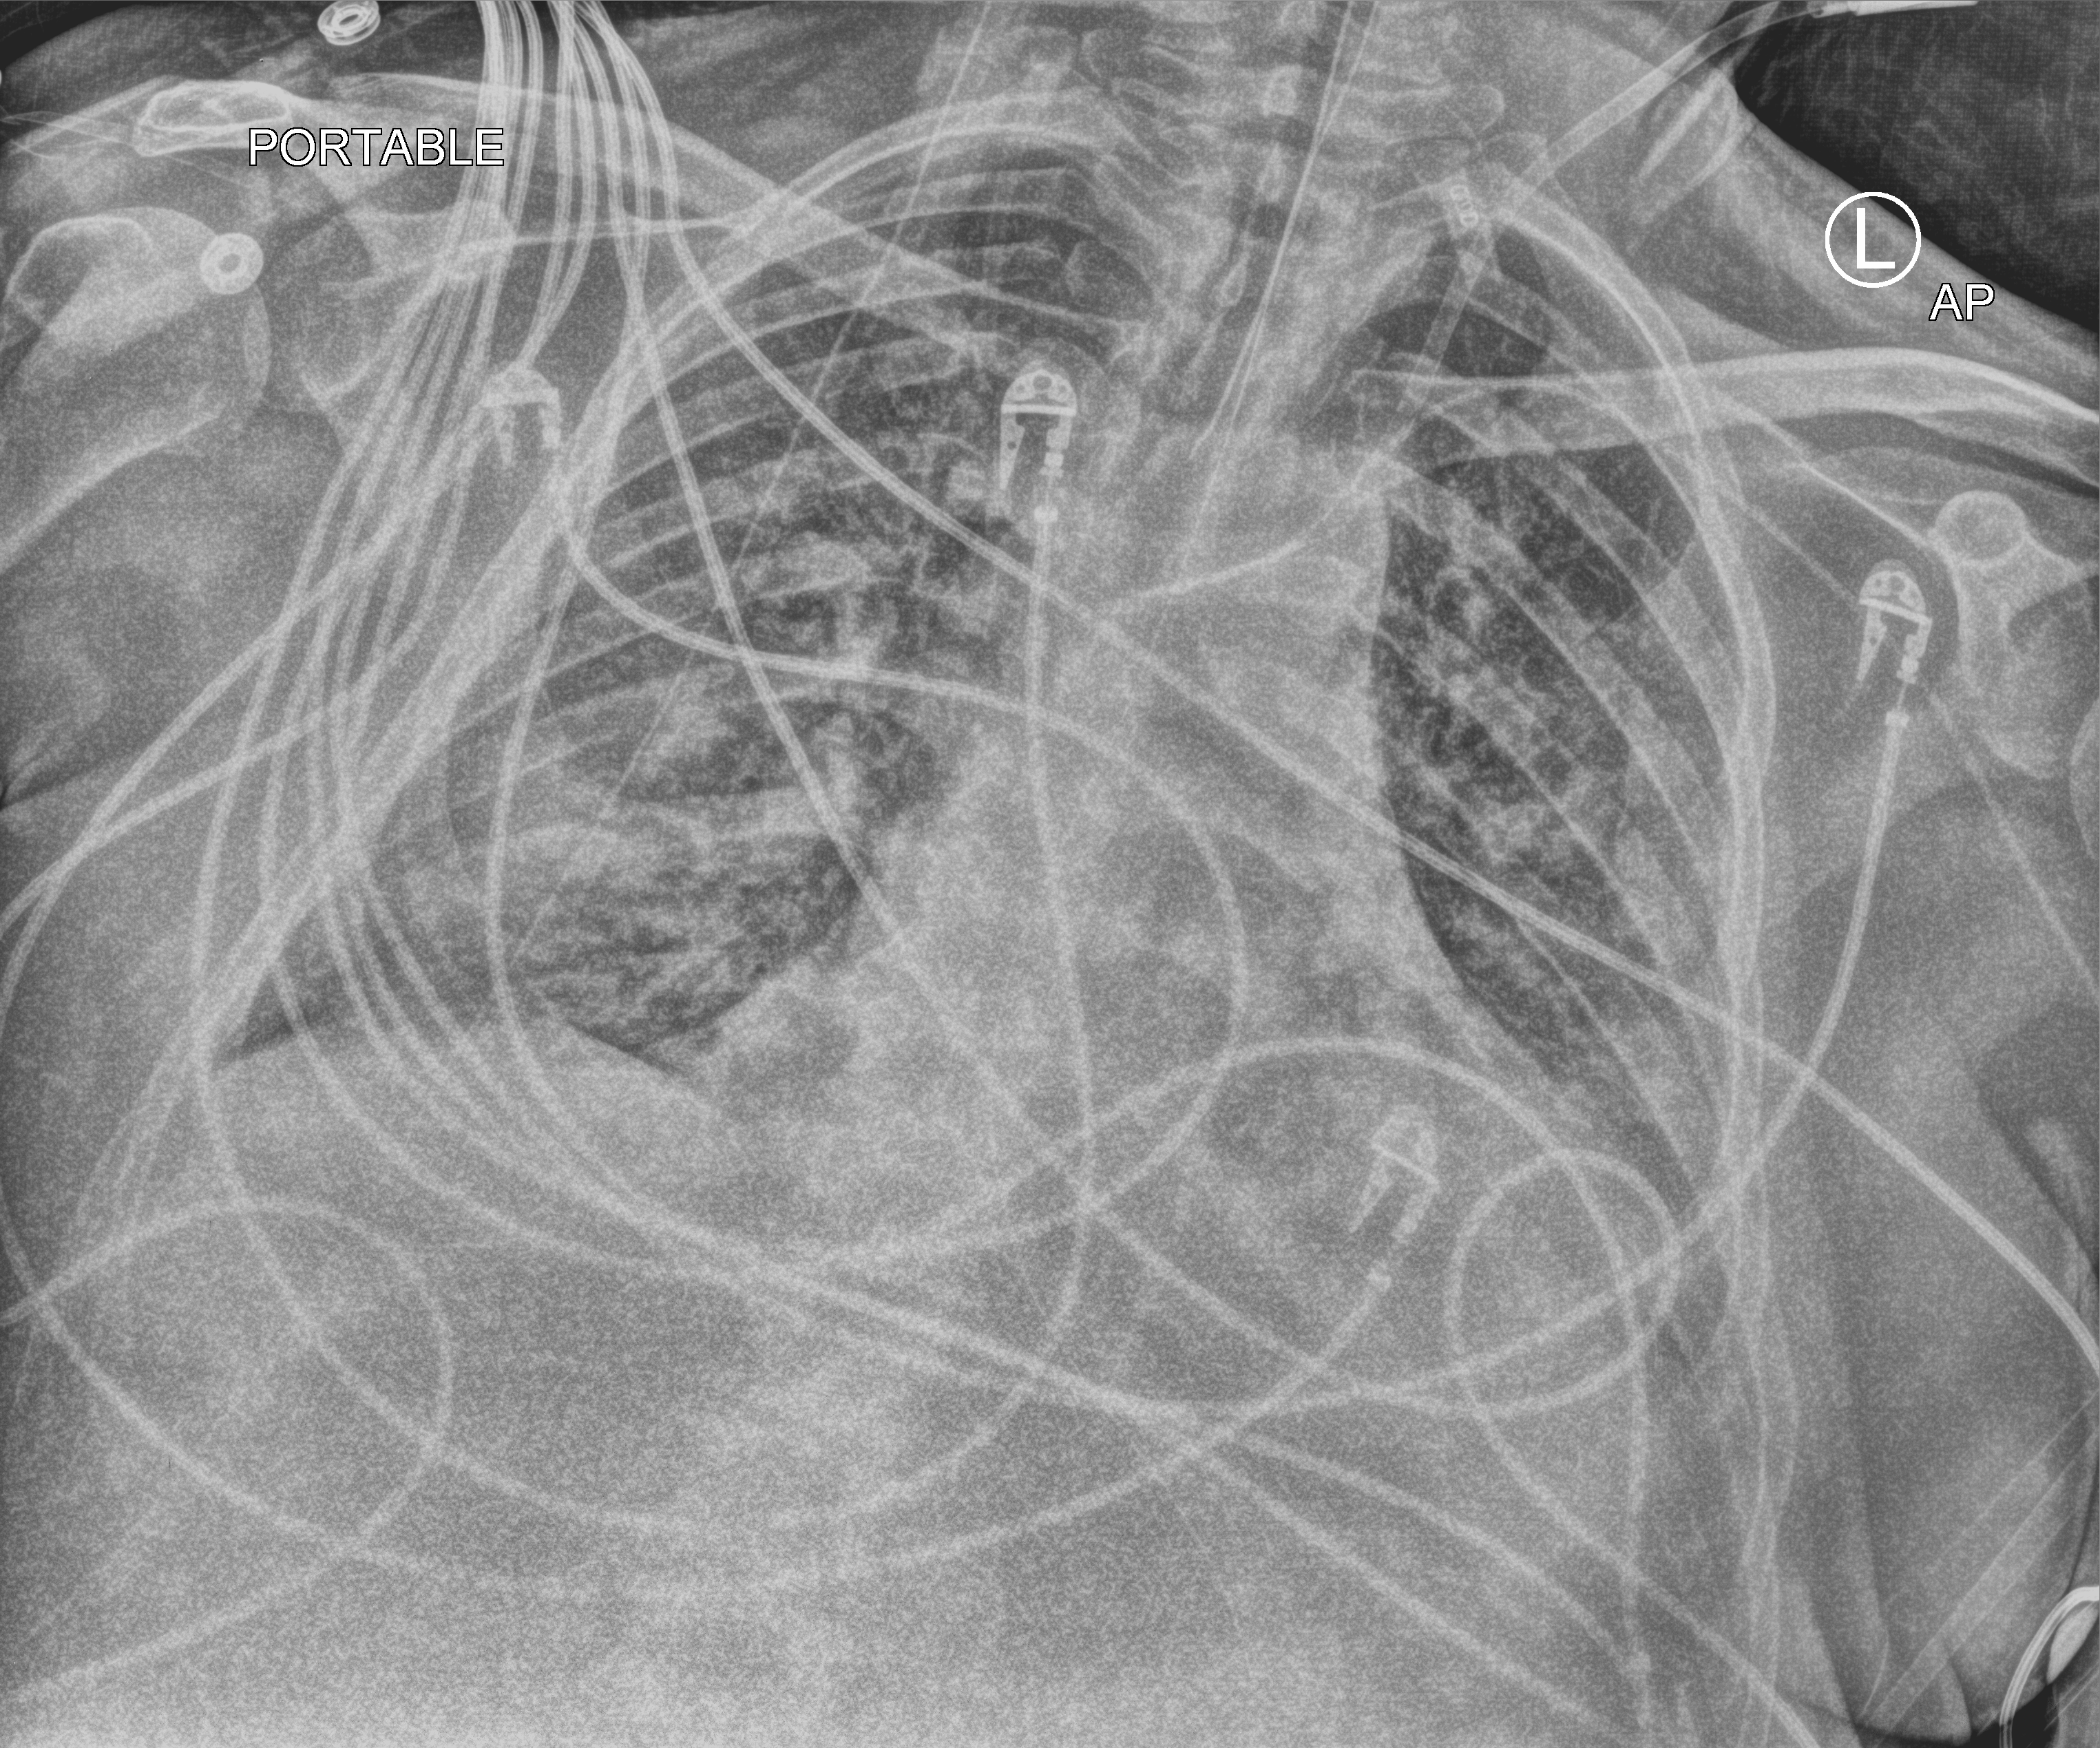
Chest X-ray (portable). Patient hospitalised with COVID-19; male, aged 18–59 years.
Admission-level facts for this patient (not findings on this image; timing relative to this image not recorded): hypertension (admission record): yes.